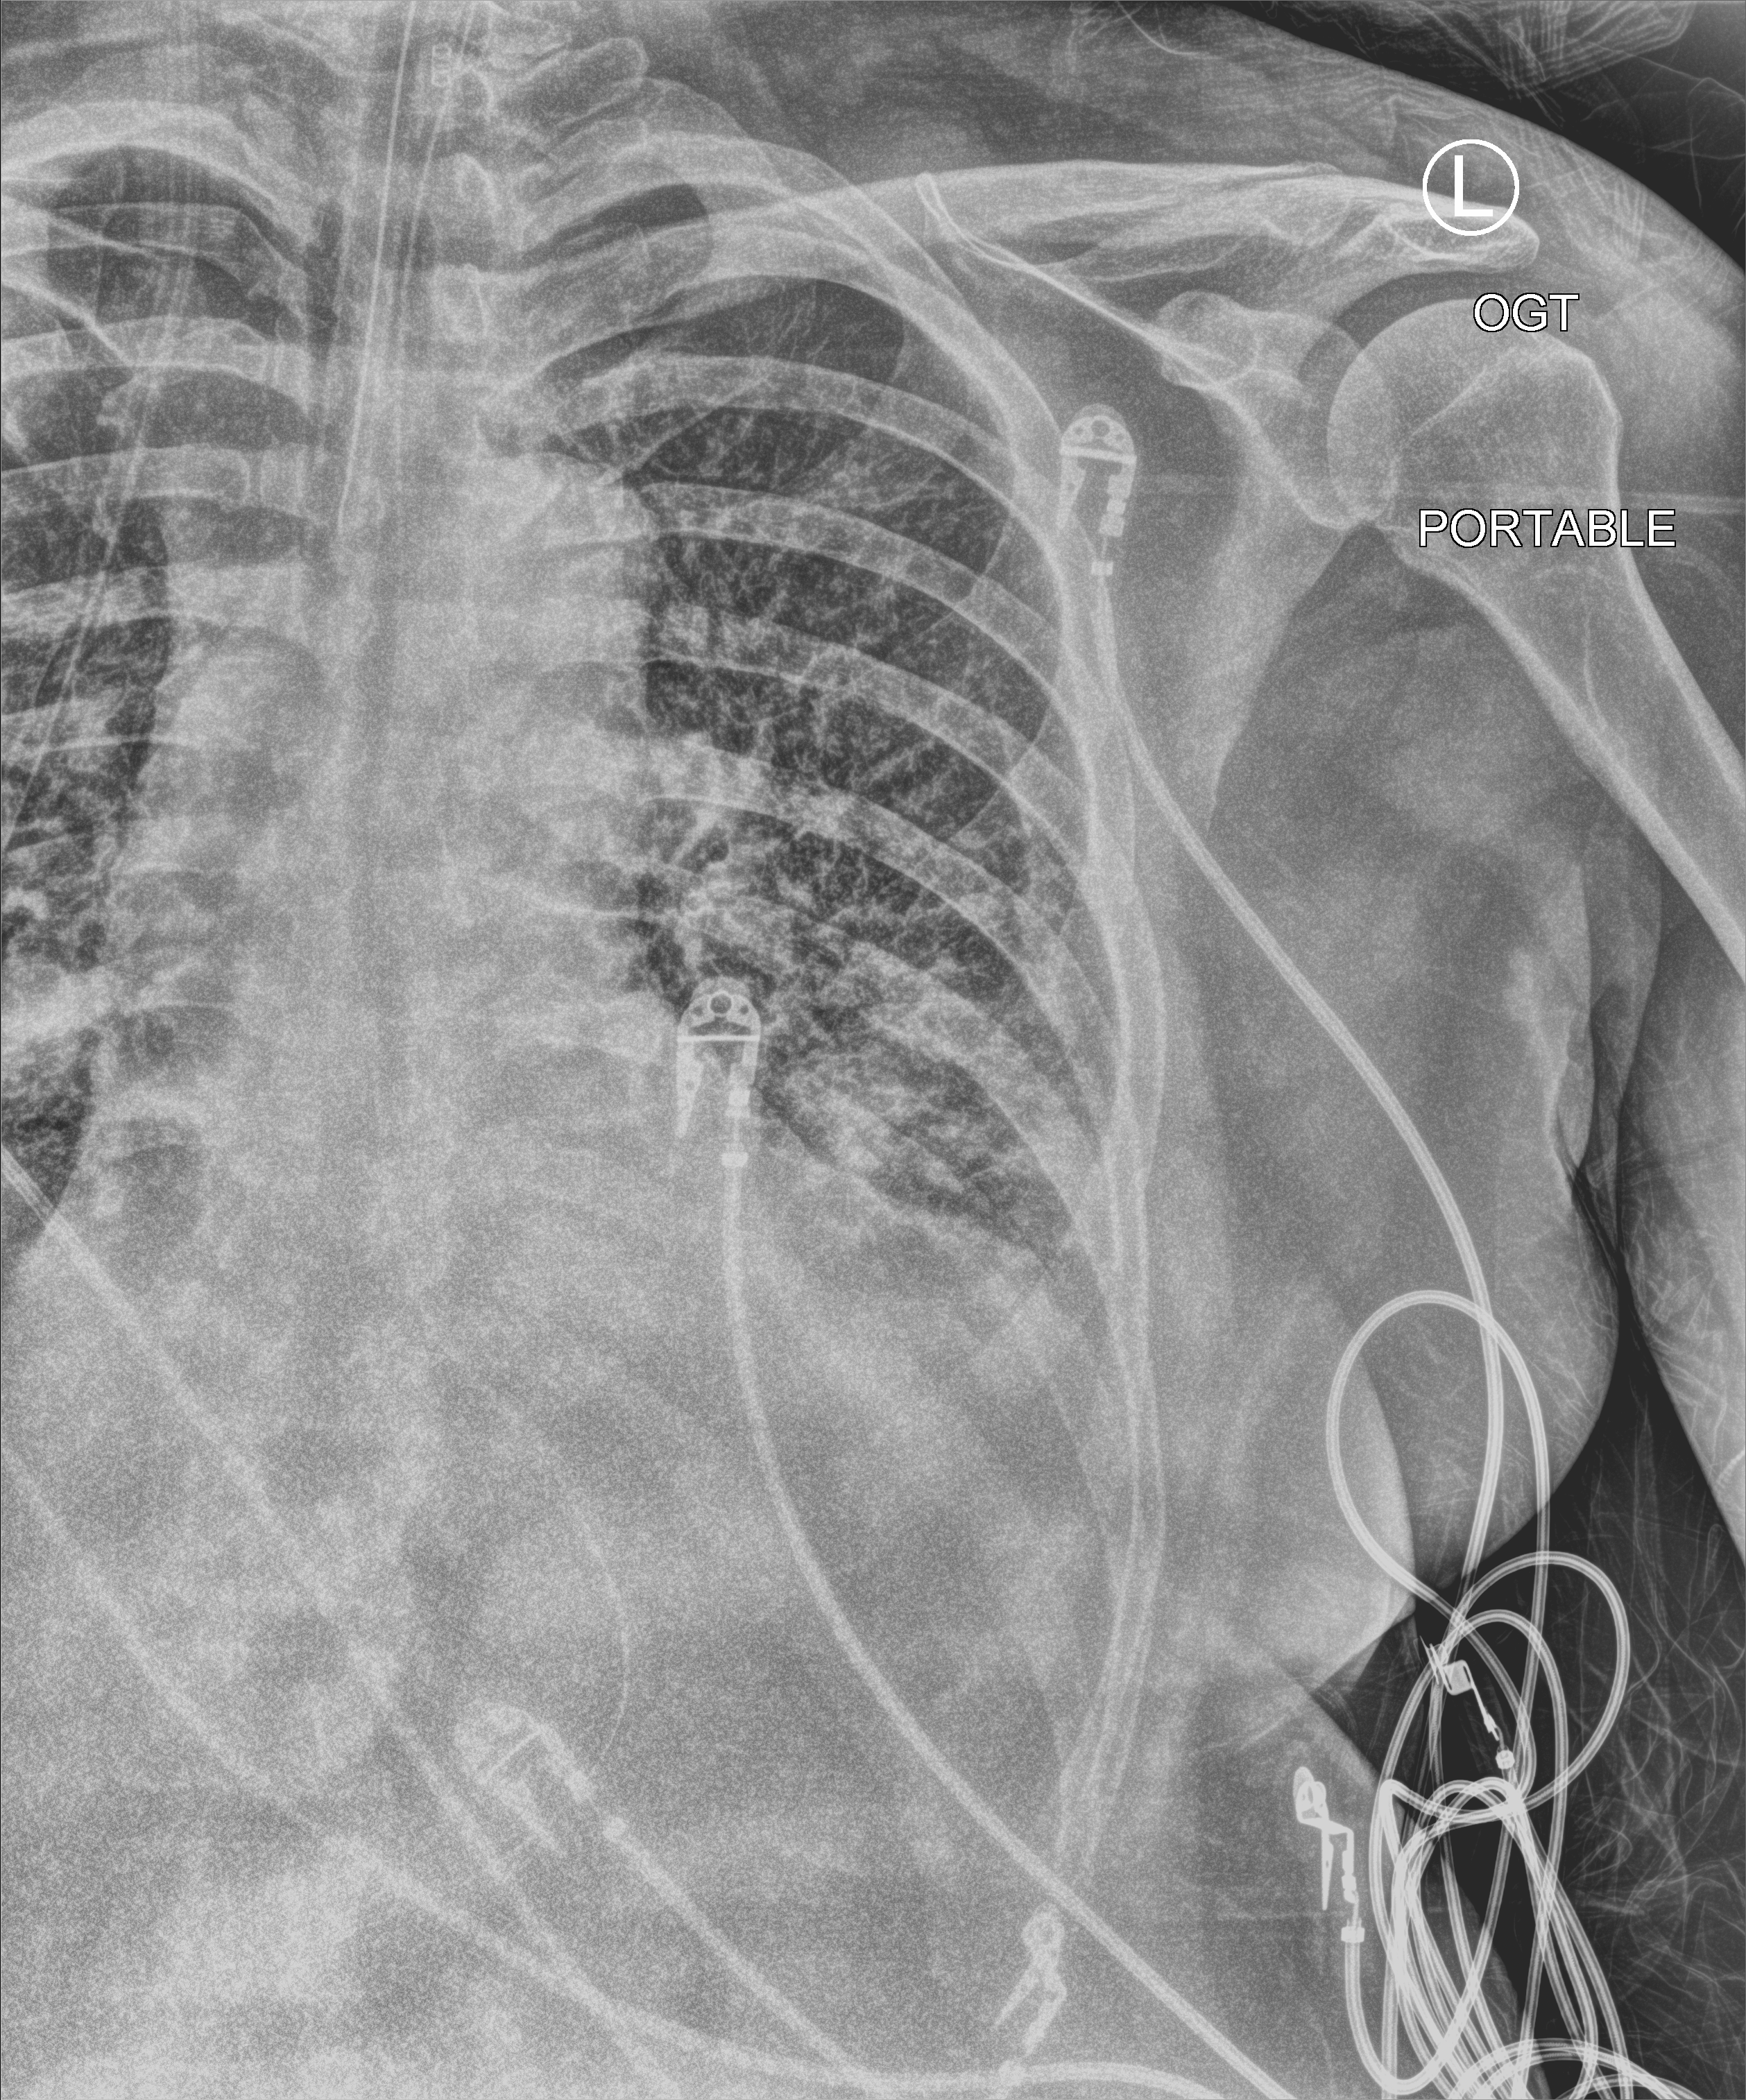
Chest X-ray (portable), anteroposterior (AP) projection. Patient hospitalised with COVID-19, aged 18–59 years.
Admission-level facts for this patient (not findings on this image; timing relative to this image not recorded):
- diabetes (admission record): no